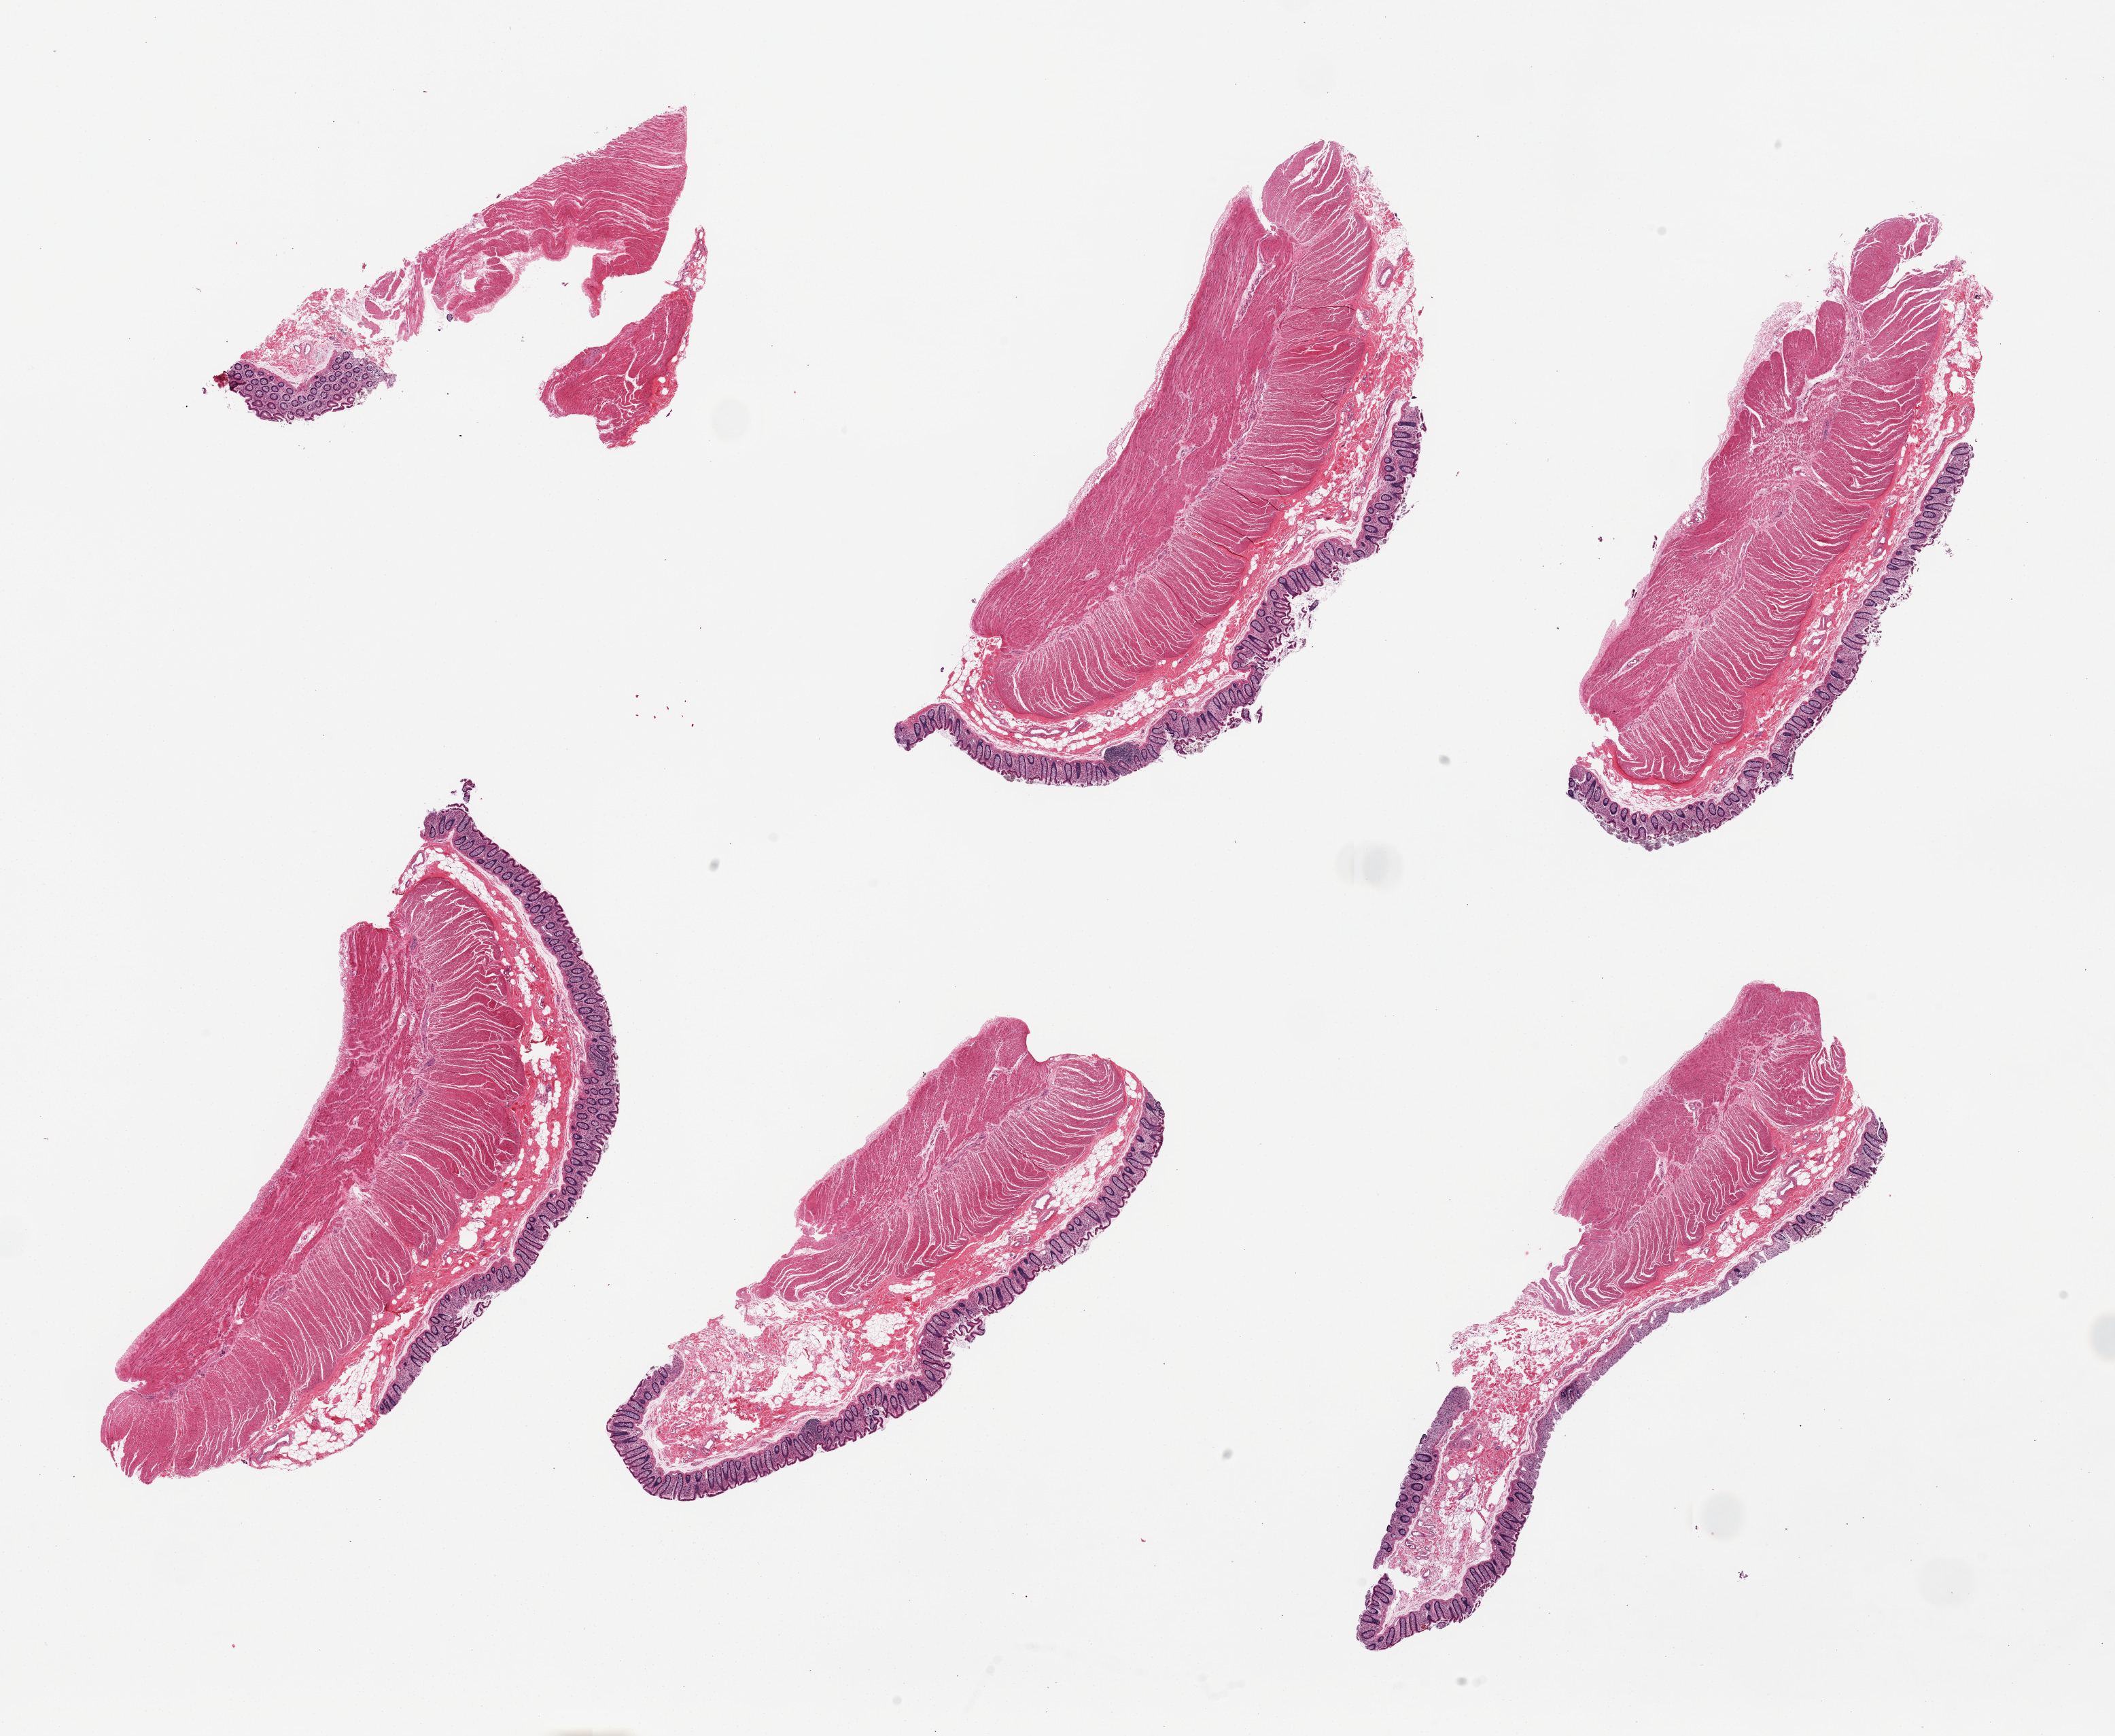
Haematoxylin and eosin whole-slide image — a low-resolution overview of the entire scanned area, about 24.6 x 20.2 mm (acquisition: 20x scan), PAXgene-fixed, paraffin-embedded tissue, target tissue: transverse colon, donor tissue sample. Donor sex: female.
Reviewer comment on this tissue sample: 6 pieces, up to 9x4mm. Well trimmed full thickness specimen. Slight surface sloughing.